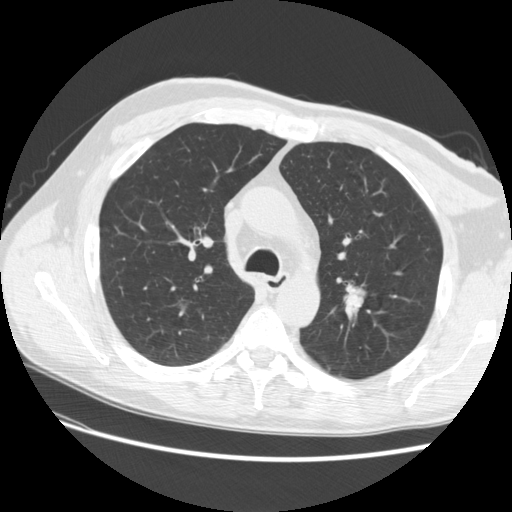
Low-dose screening chest CT, one axial slice. Position 179 of 256 along the scan axis. 120 kVp. Lung window (W 1500 / L -600 HU). 512 × 512 image matrix, field of view 366 × 366 mm.
Structures marked on this image (manually delineated by an expert):
- lesion 1 (tumor, upper lobe of left lung): bounding box [x1, y1, x2, y2] px = [345, 290, 364, 313]